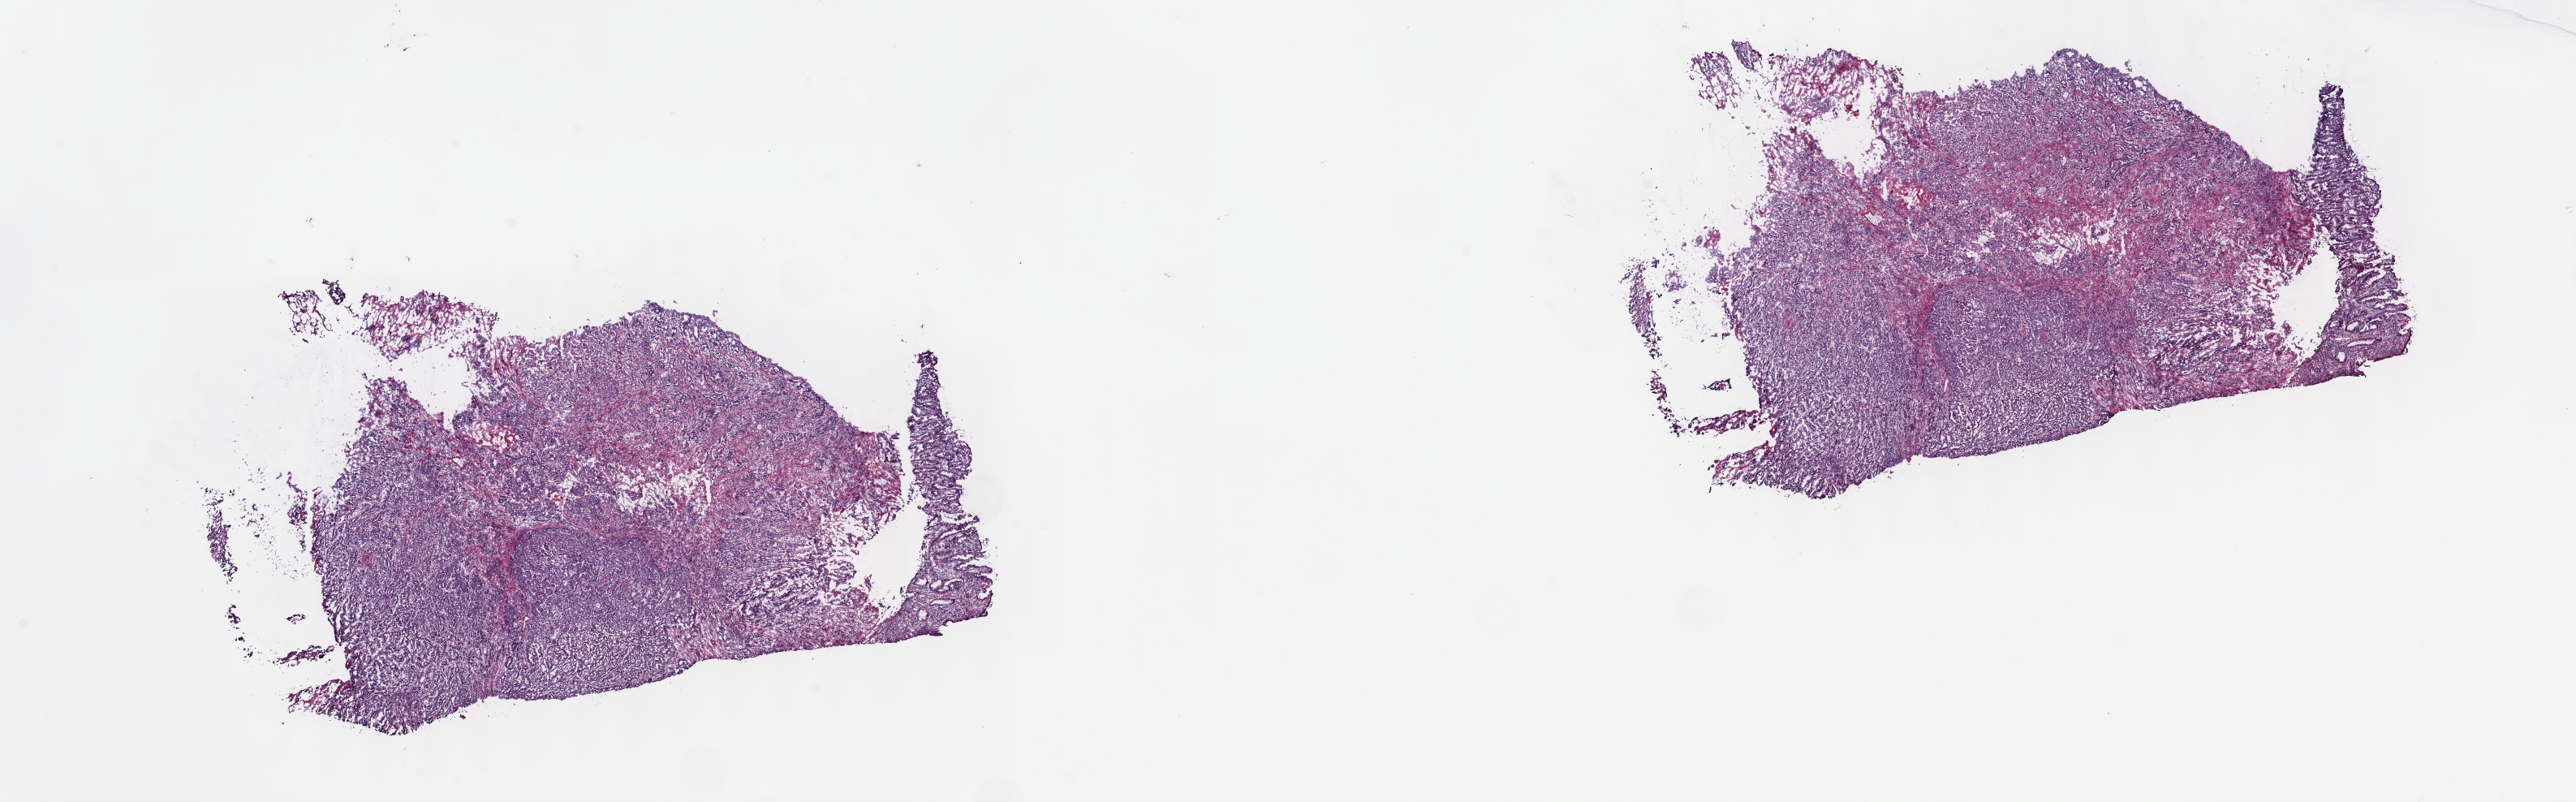
Digitized H&E tissue section (whole slide) — a low-resolution overview of the entire scanned area, about 25.7 x 8.0 mm (acquisition: 40x scan), frozen section from the top of the tissue portion, stomach, primary tumour sample. Patient: male, age at initial diagnosis 78 years. Histologic grade: G3 (poorly differentiated). Pathologist review of this section (percent, as recorded): tumour cells 80%, tumour nuclei 80%, normal cells 0%, stromal cells 20%, necrosis 0%. Inflammatory infiltration, as recorded: lymphocyte infiltration 2%, monocyte infiltration 1%, neutrophil infiltration 3%.
Histologic diagnosis: Tubular adenocarcinoma (cardia, NOS). AJCC pathologic stage: IIIB.